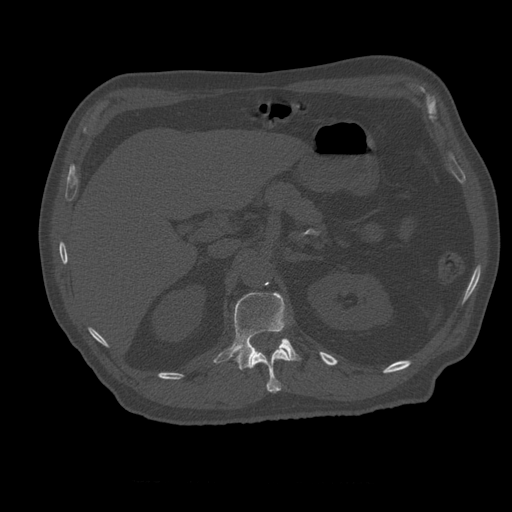
CT including the spine, one axial slice; position 247 of 399 along the scan axis; reconstruction kernel STANDARD; bone window (W 1800 / L 400 HU); 512 × 512 image matrix, field of view 407 × 407 mm. Patient age 73 years. From the clinical record (not read from this slice): primary cancer: prostate; vertebrae with lytic lesions (as recorded): L2.
Outlined on this slice (semi-automatic segmentation, software-assisted and operator-edited):
- L1 vertebra: bounding box (x1, y1, x2, y2) in pixels: (214, 293, 301, 370)
- T12 vertebra: (249, 348, 290, 393)